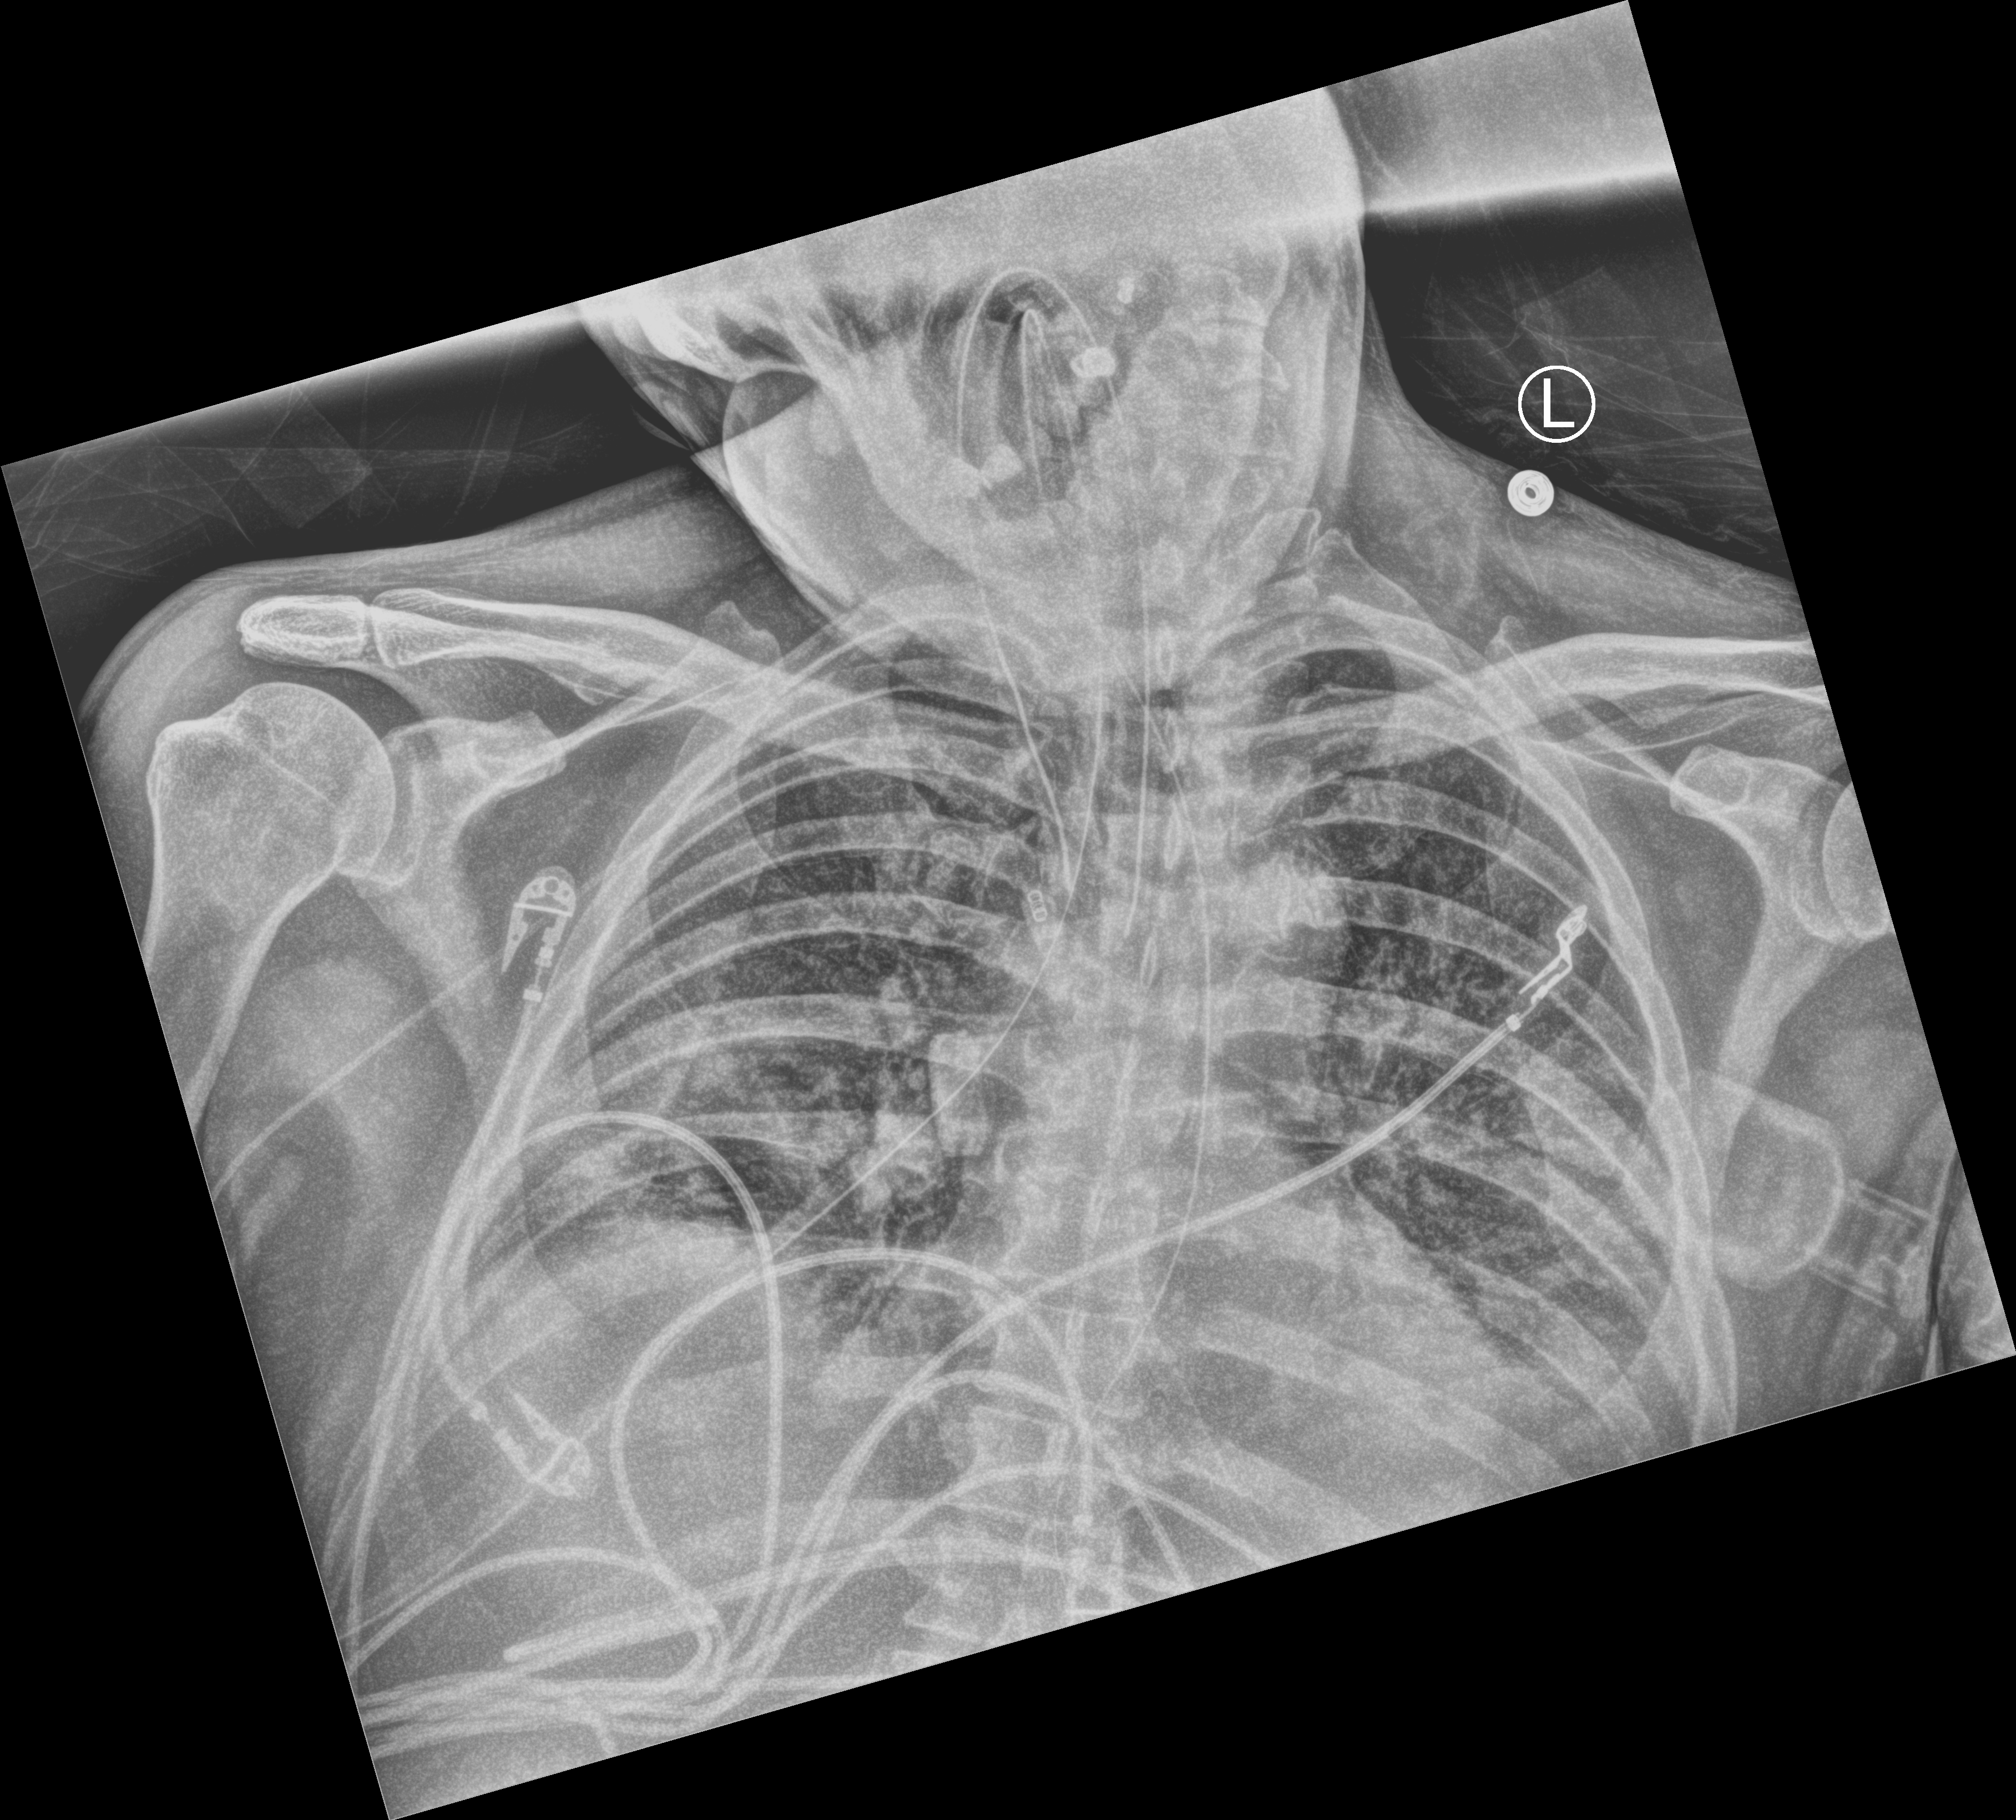
Portable chest radiograph, anteroposterior (AP) projection. Male patient hospitalised with COVID-19, age 60–74 years.
Admission-level facts for this patient (not findings on this image; timing relative to this image not recorded):
- mechanically ventilated during this hospital stay: yes